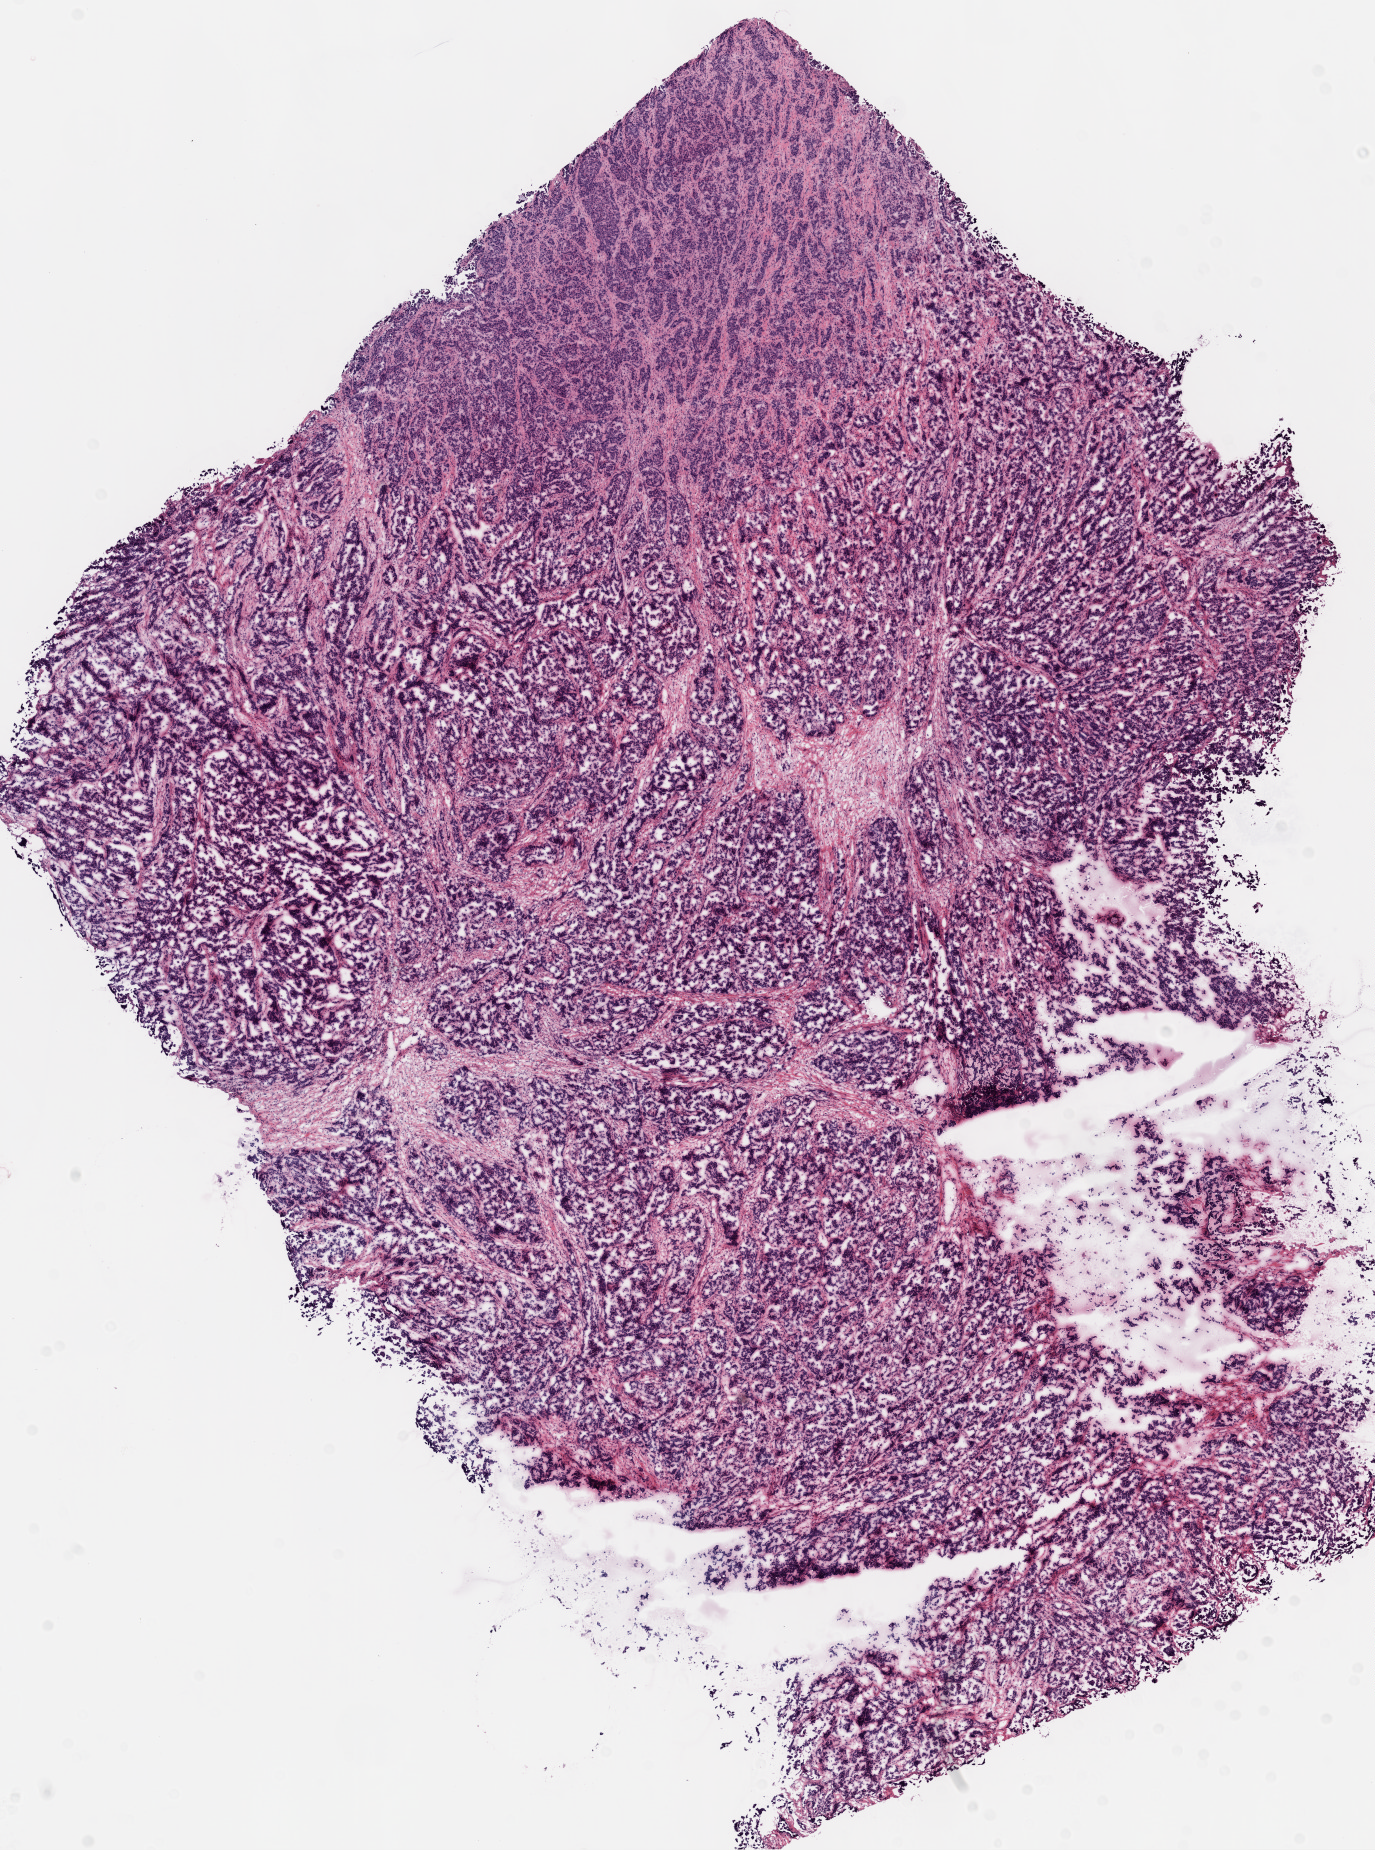
Hematoxylin and eosin (H&E) stained whole-slide image — shown as a low-resolution overview of the whole scanned area (about 11.0 x 14.8 mm), frozen section from the top of the tissue portion, ovary, primary tumour sample. Female patient; age at initial diagnosis 48 years. Histologic grade: G3 (poorly differentiated). Slide review estimates, as recorded: tumour cells 89%, tumour nuclei 90%, normal cells 0%, stromal cells 10%, necrosis 1%.
* diagnosis: Serous cystadenocarcinoma, NOS
* FIGO stage: IIIC